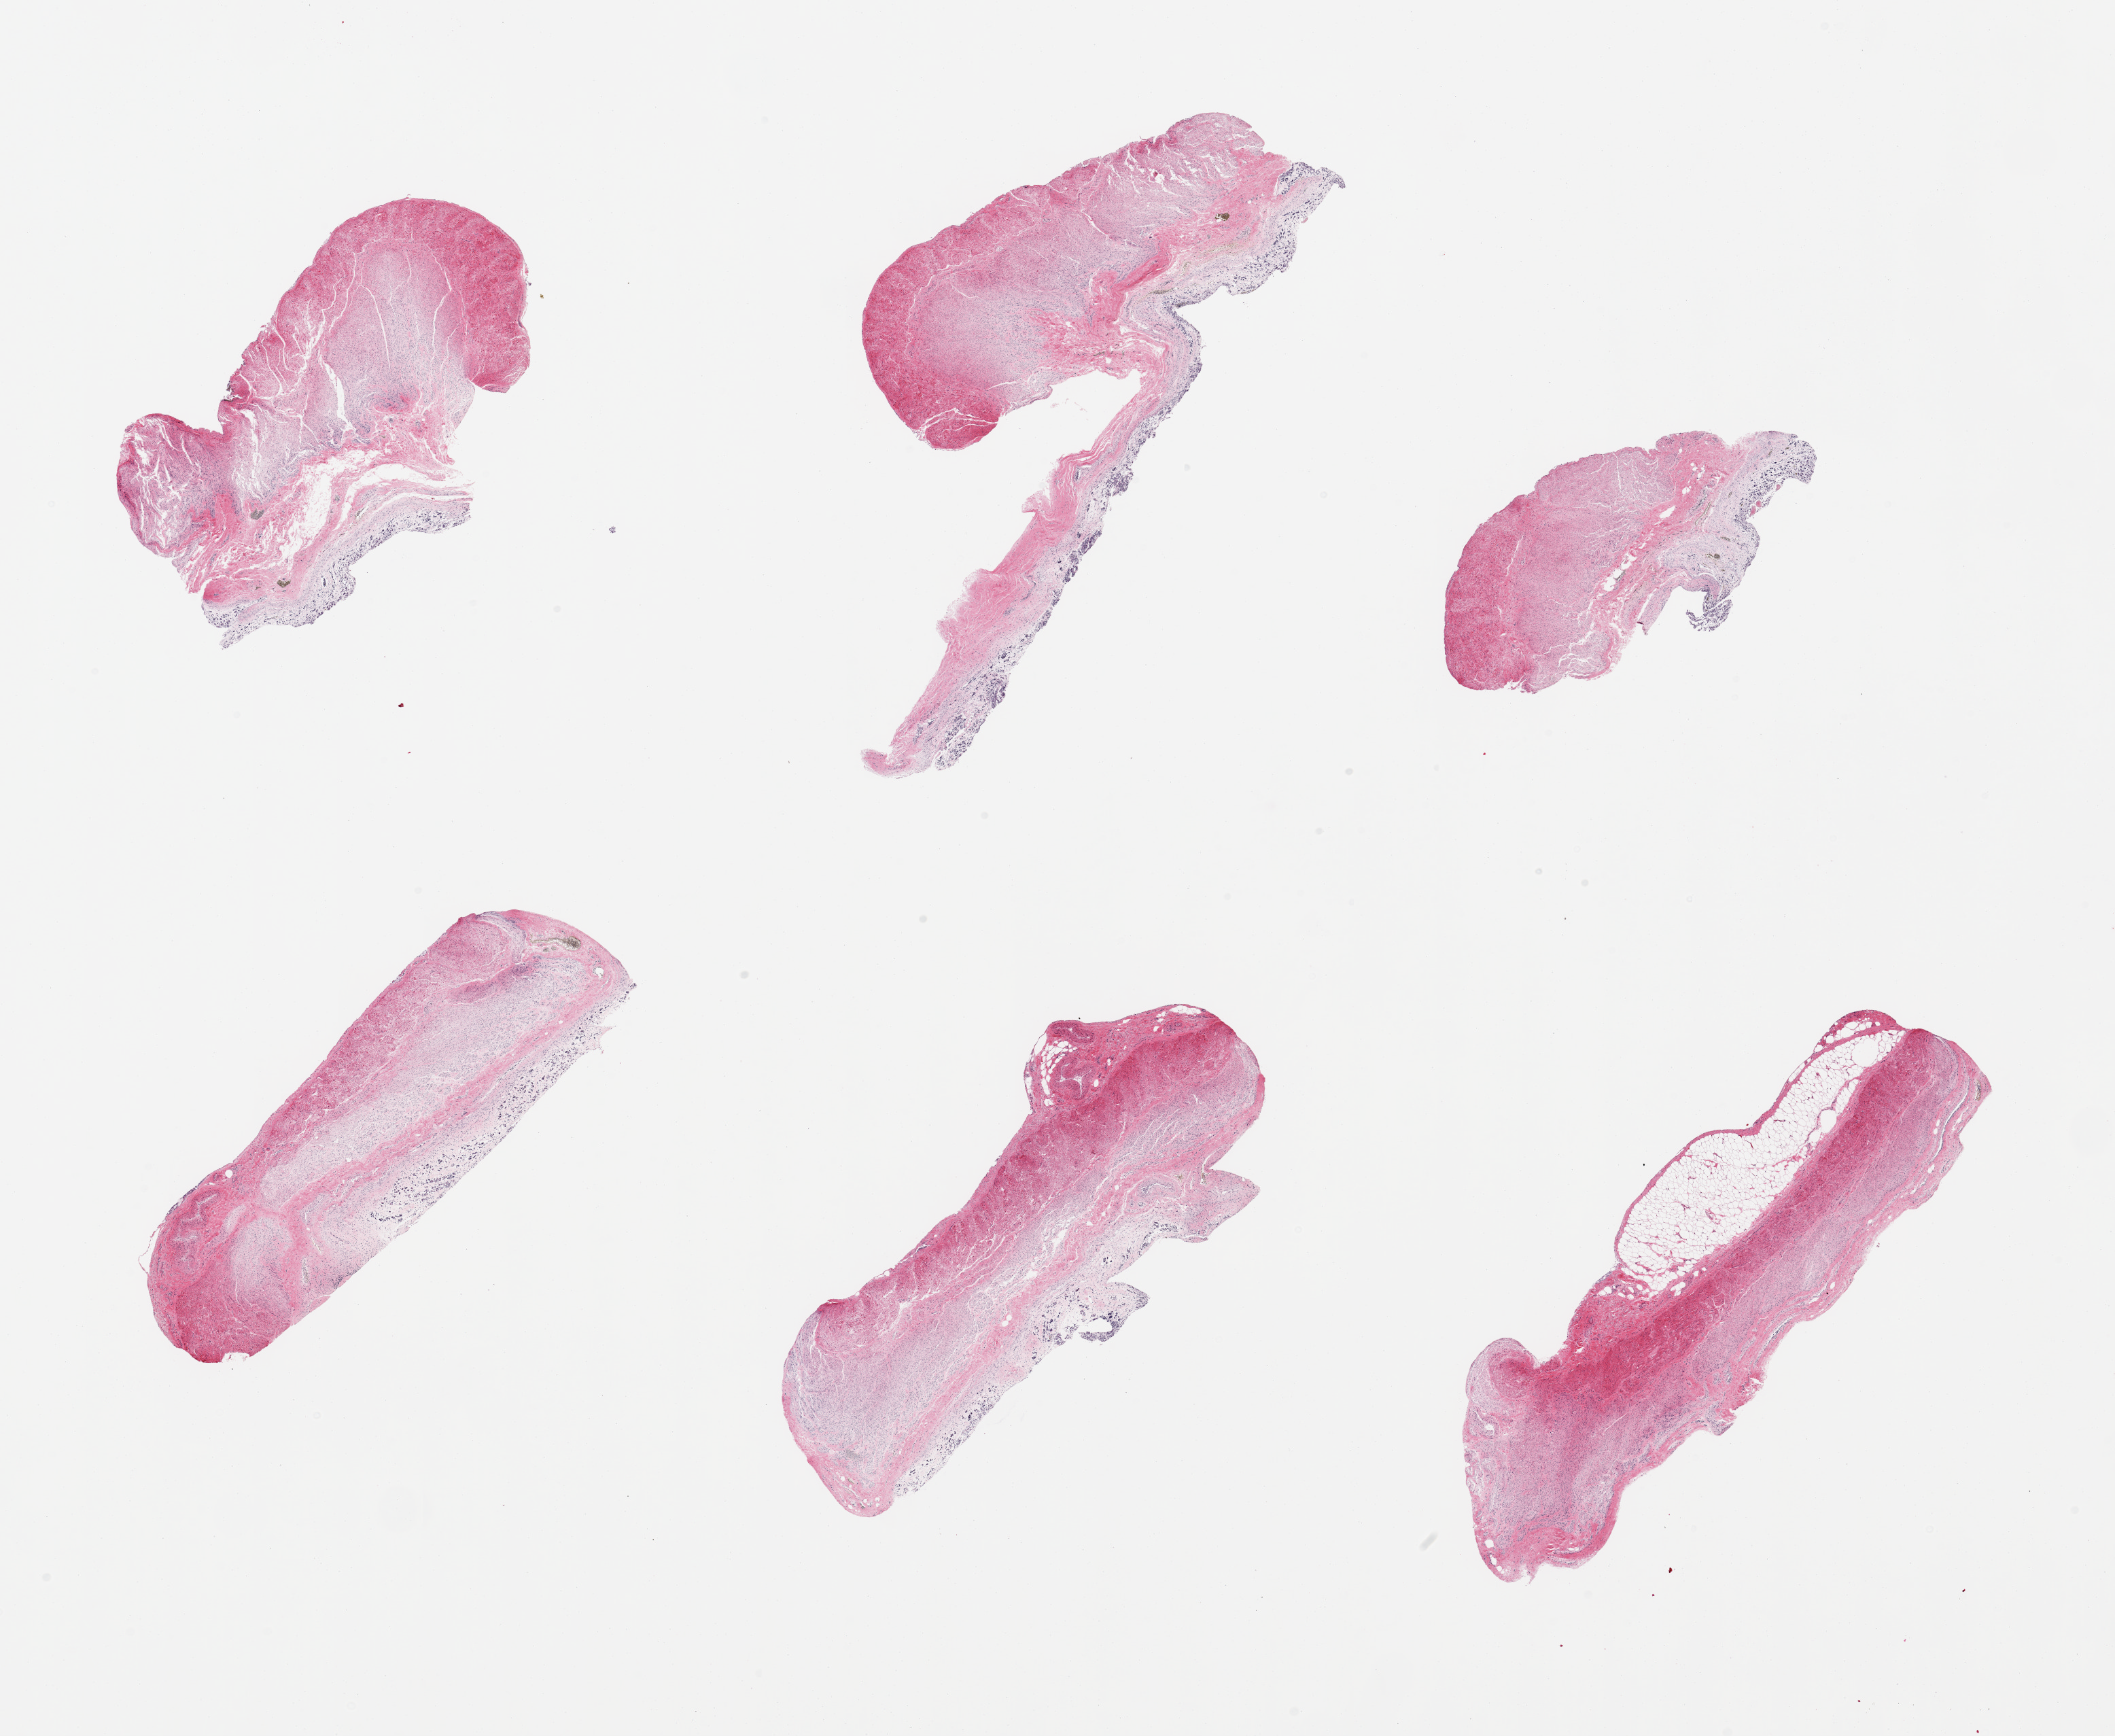
Hematoxylin and eosin (H&E) whole-slide image, brightfield — whole scanned area (about 24.6 x 20.2 mm, slide scanned at 20x) shown as a low-resolution overview; PAXgene-fixed paraffin-embedded (PFPE) section; section of gastroesophageal junction (target tissue); tissue donor sample. Donor sex: male.
Review note (as recorded): 6 pieces, unusually advanced autolysis.